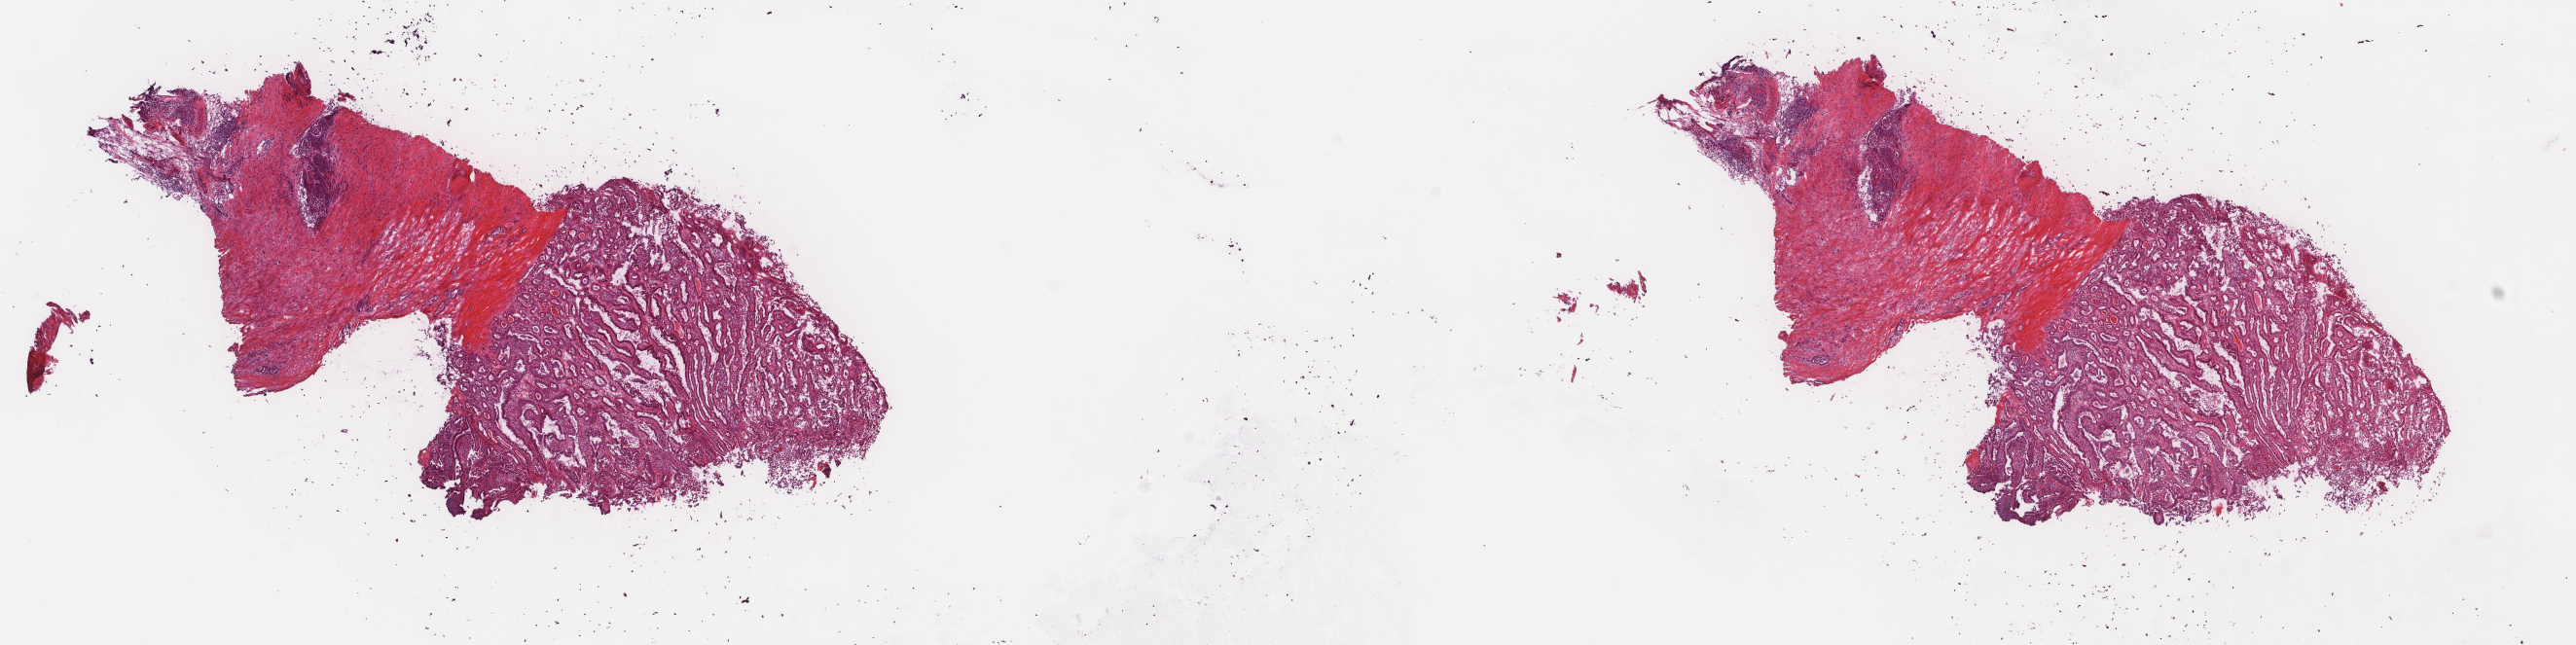
Whole-slide histology image, Hematoxylin and eosin (H&E) stained — shown as a low-resolution overview of the whole scanned area (about 21.0 x 5.3 mm, acquisition: 40x scan). Frozen section. Metastatic tumour sample, sampled site not recorded. Patient: male, age at initial diagnosis 33 years. Composition of this section per pathologist review: tumour cells 70%, tumour nuclei 70%, normal cells 0%, stromal cells 30%, necrosis 0%. Inflammatory infiltration, as recorded: lymphocyte infiltration 10%, monocyte infiltration 0%, neutrophil infiltration 0%.
- this section: metastatic tumour tissue
- patient diagnosis: Papillary adenocarcinoma, NOS (primary site: thyroid gland)